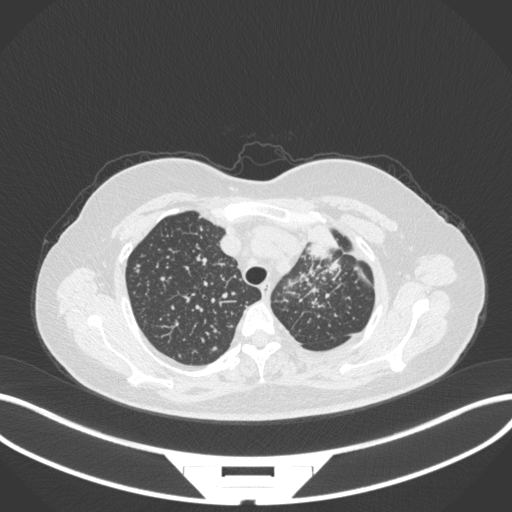
Chest CT, one axial slice. Position 268 of 348 along the scan axis. Reconstruction kernel B31f. Lung window (W 1500 / L -600 HU). 1 mm slice thickness. 512 × 512 image matrix, field of view 400 × 400 mm. Patient: female, 49 years. From the clinical record (not read from this slice): clinical TNM (as recorded): T1c N0 M1.
Annotated regions visible in this slice (rectangle marked by the reading radiologist):
- lung tumour (recorded histology: adenocarcinoma): box from (x=305, y=219) to (x=343, y=262) px